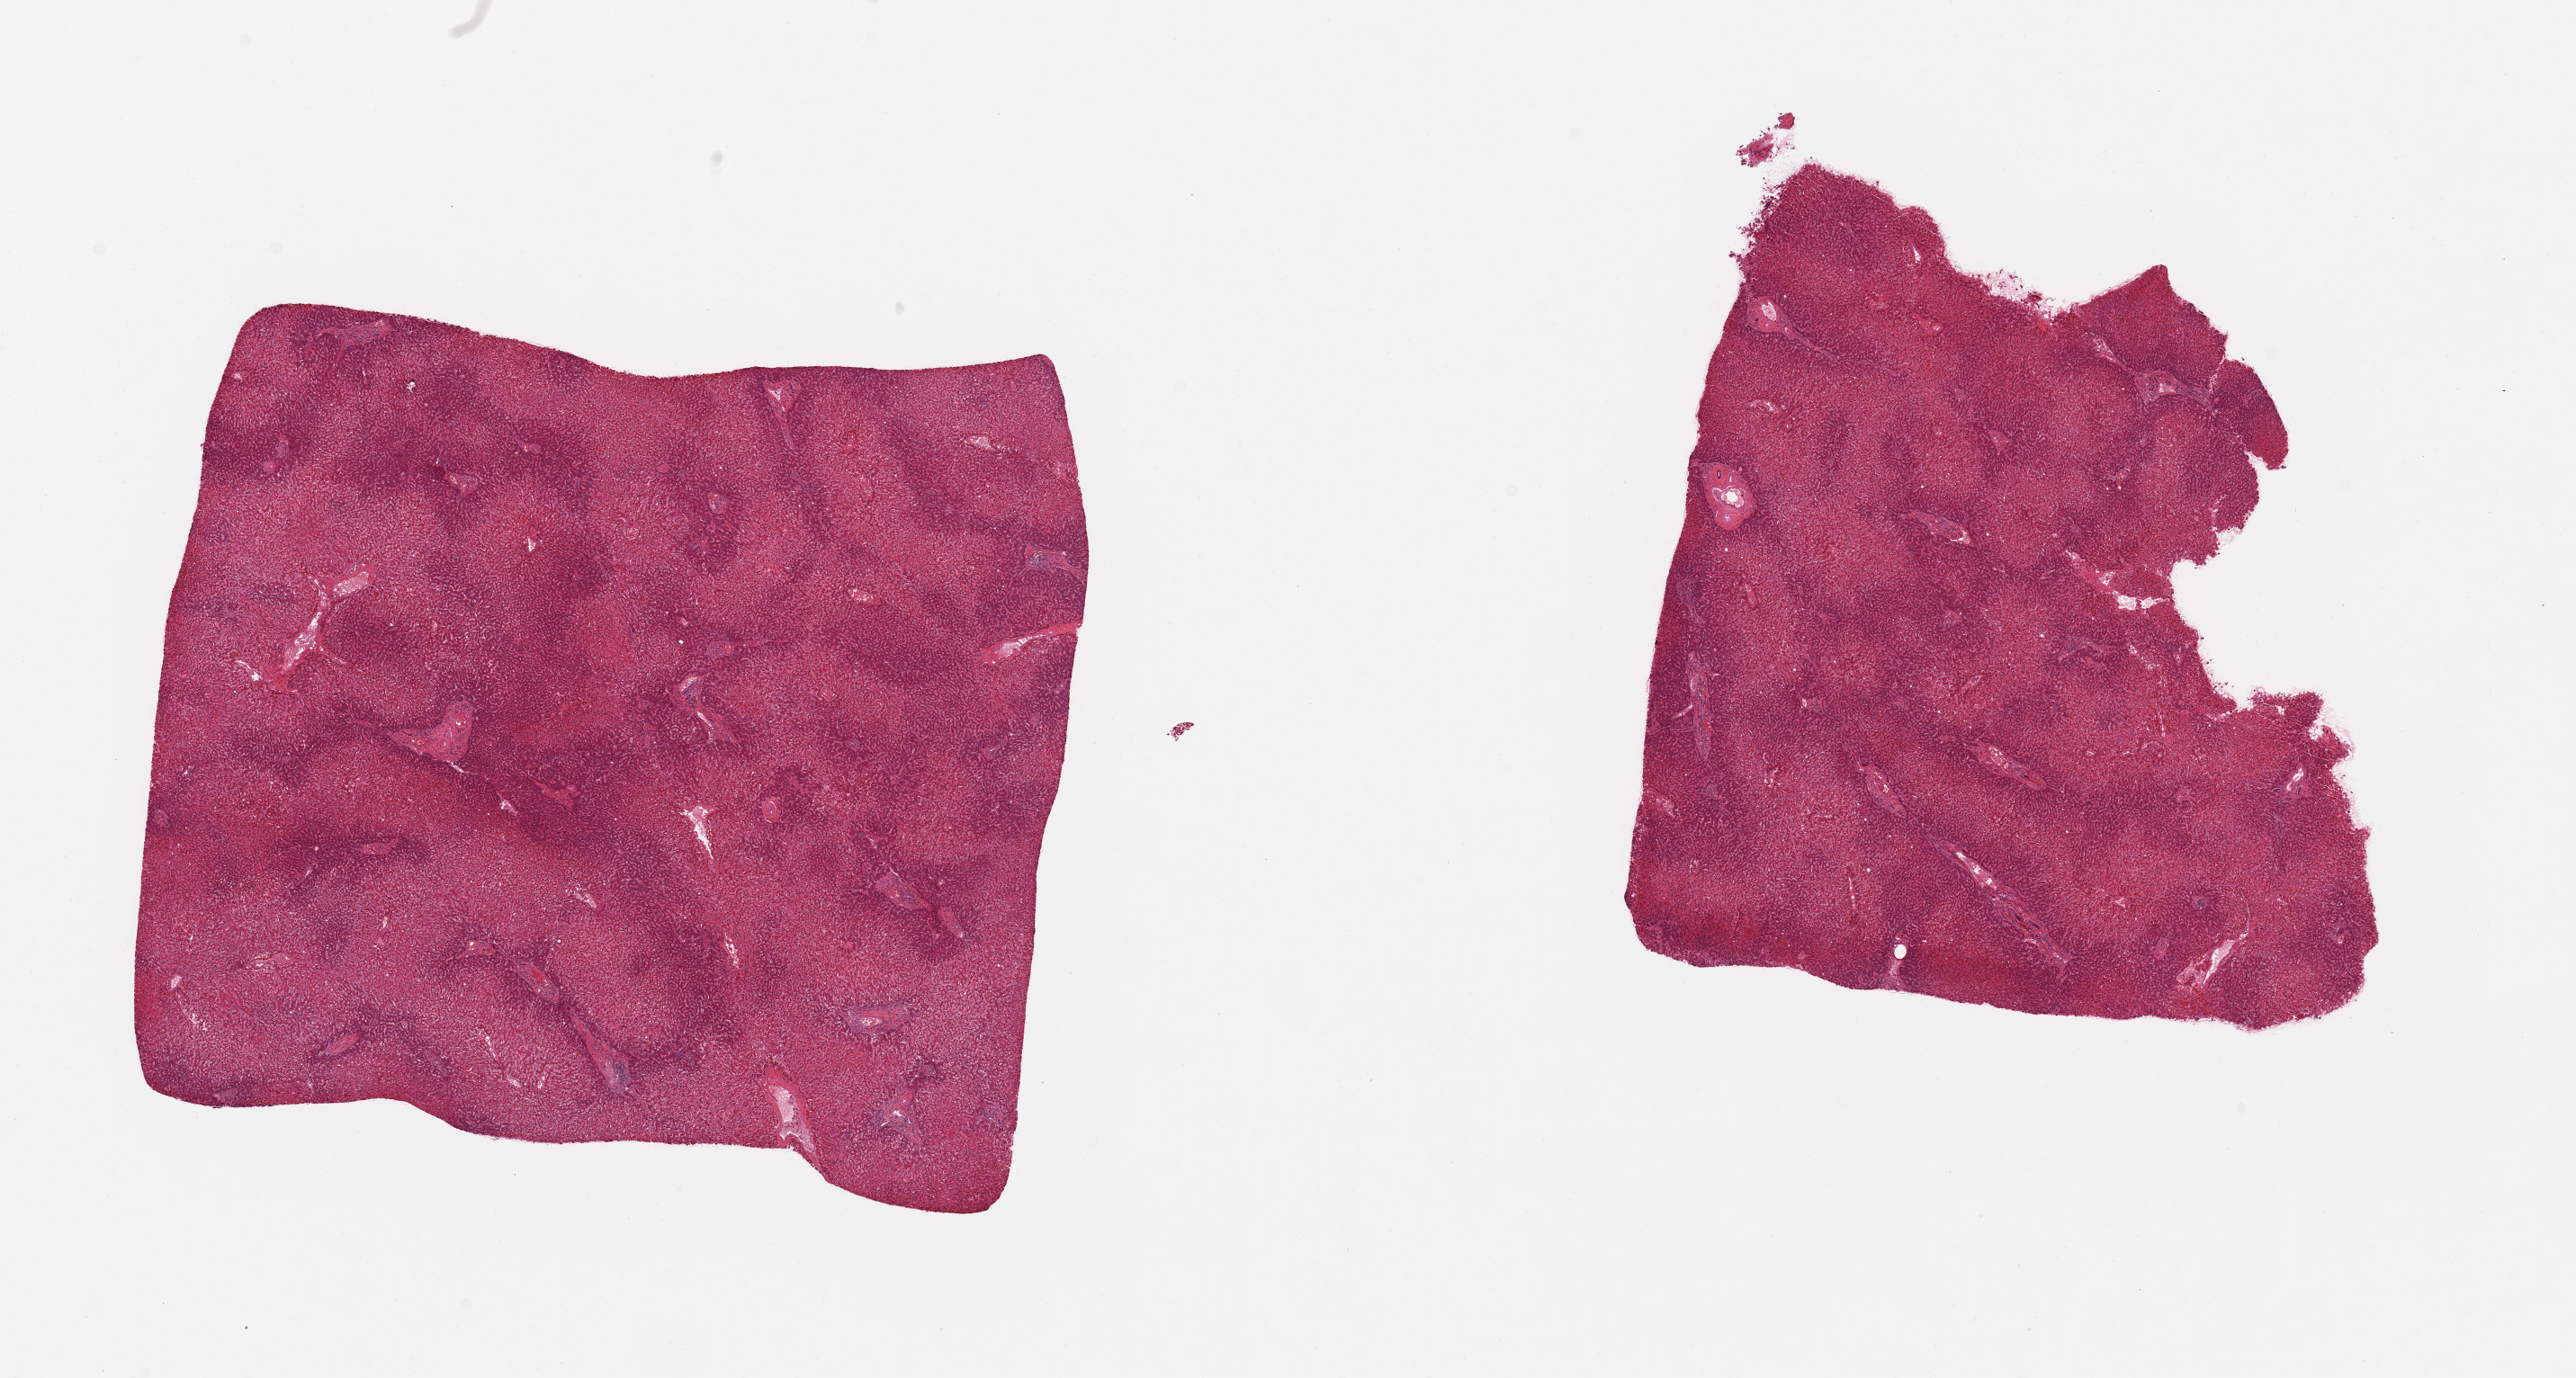
H&E whole-slide image — shown as a low-resolution overview of the whole scanned area (about 22.6 x 12.1 mm), PAXgene-fixed paraffin-embedded (PFPE) section, sampled site (target tissue): liver, donor tissue sample. Donor sex: male.
* review note (as recorded): 2 pieces; mild central degeneration